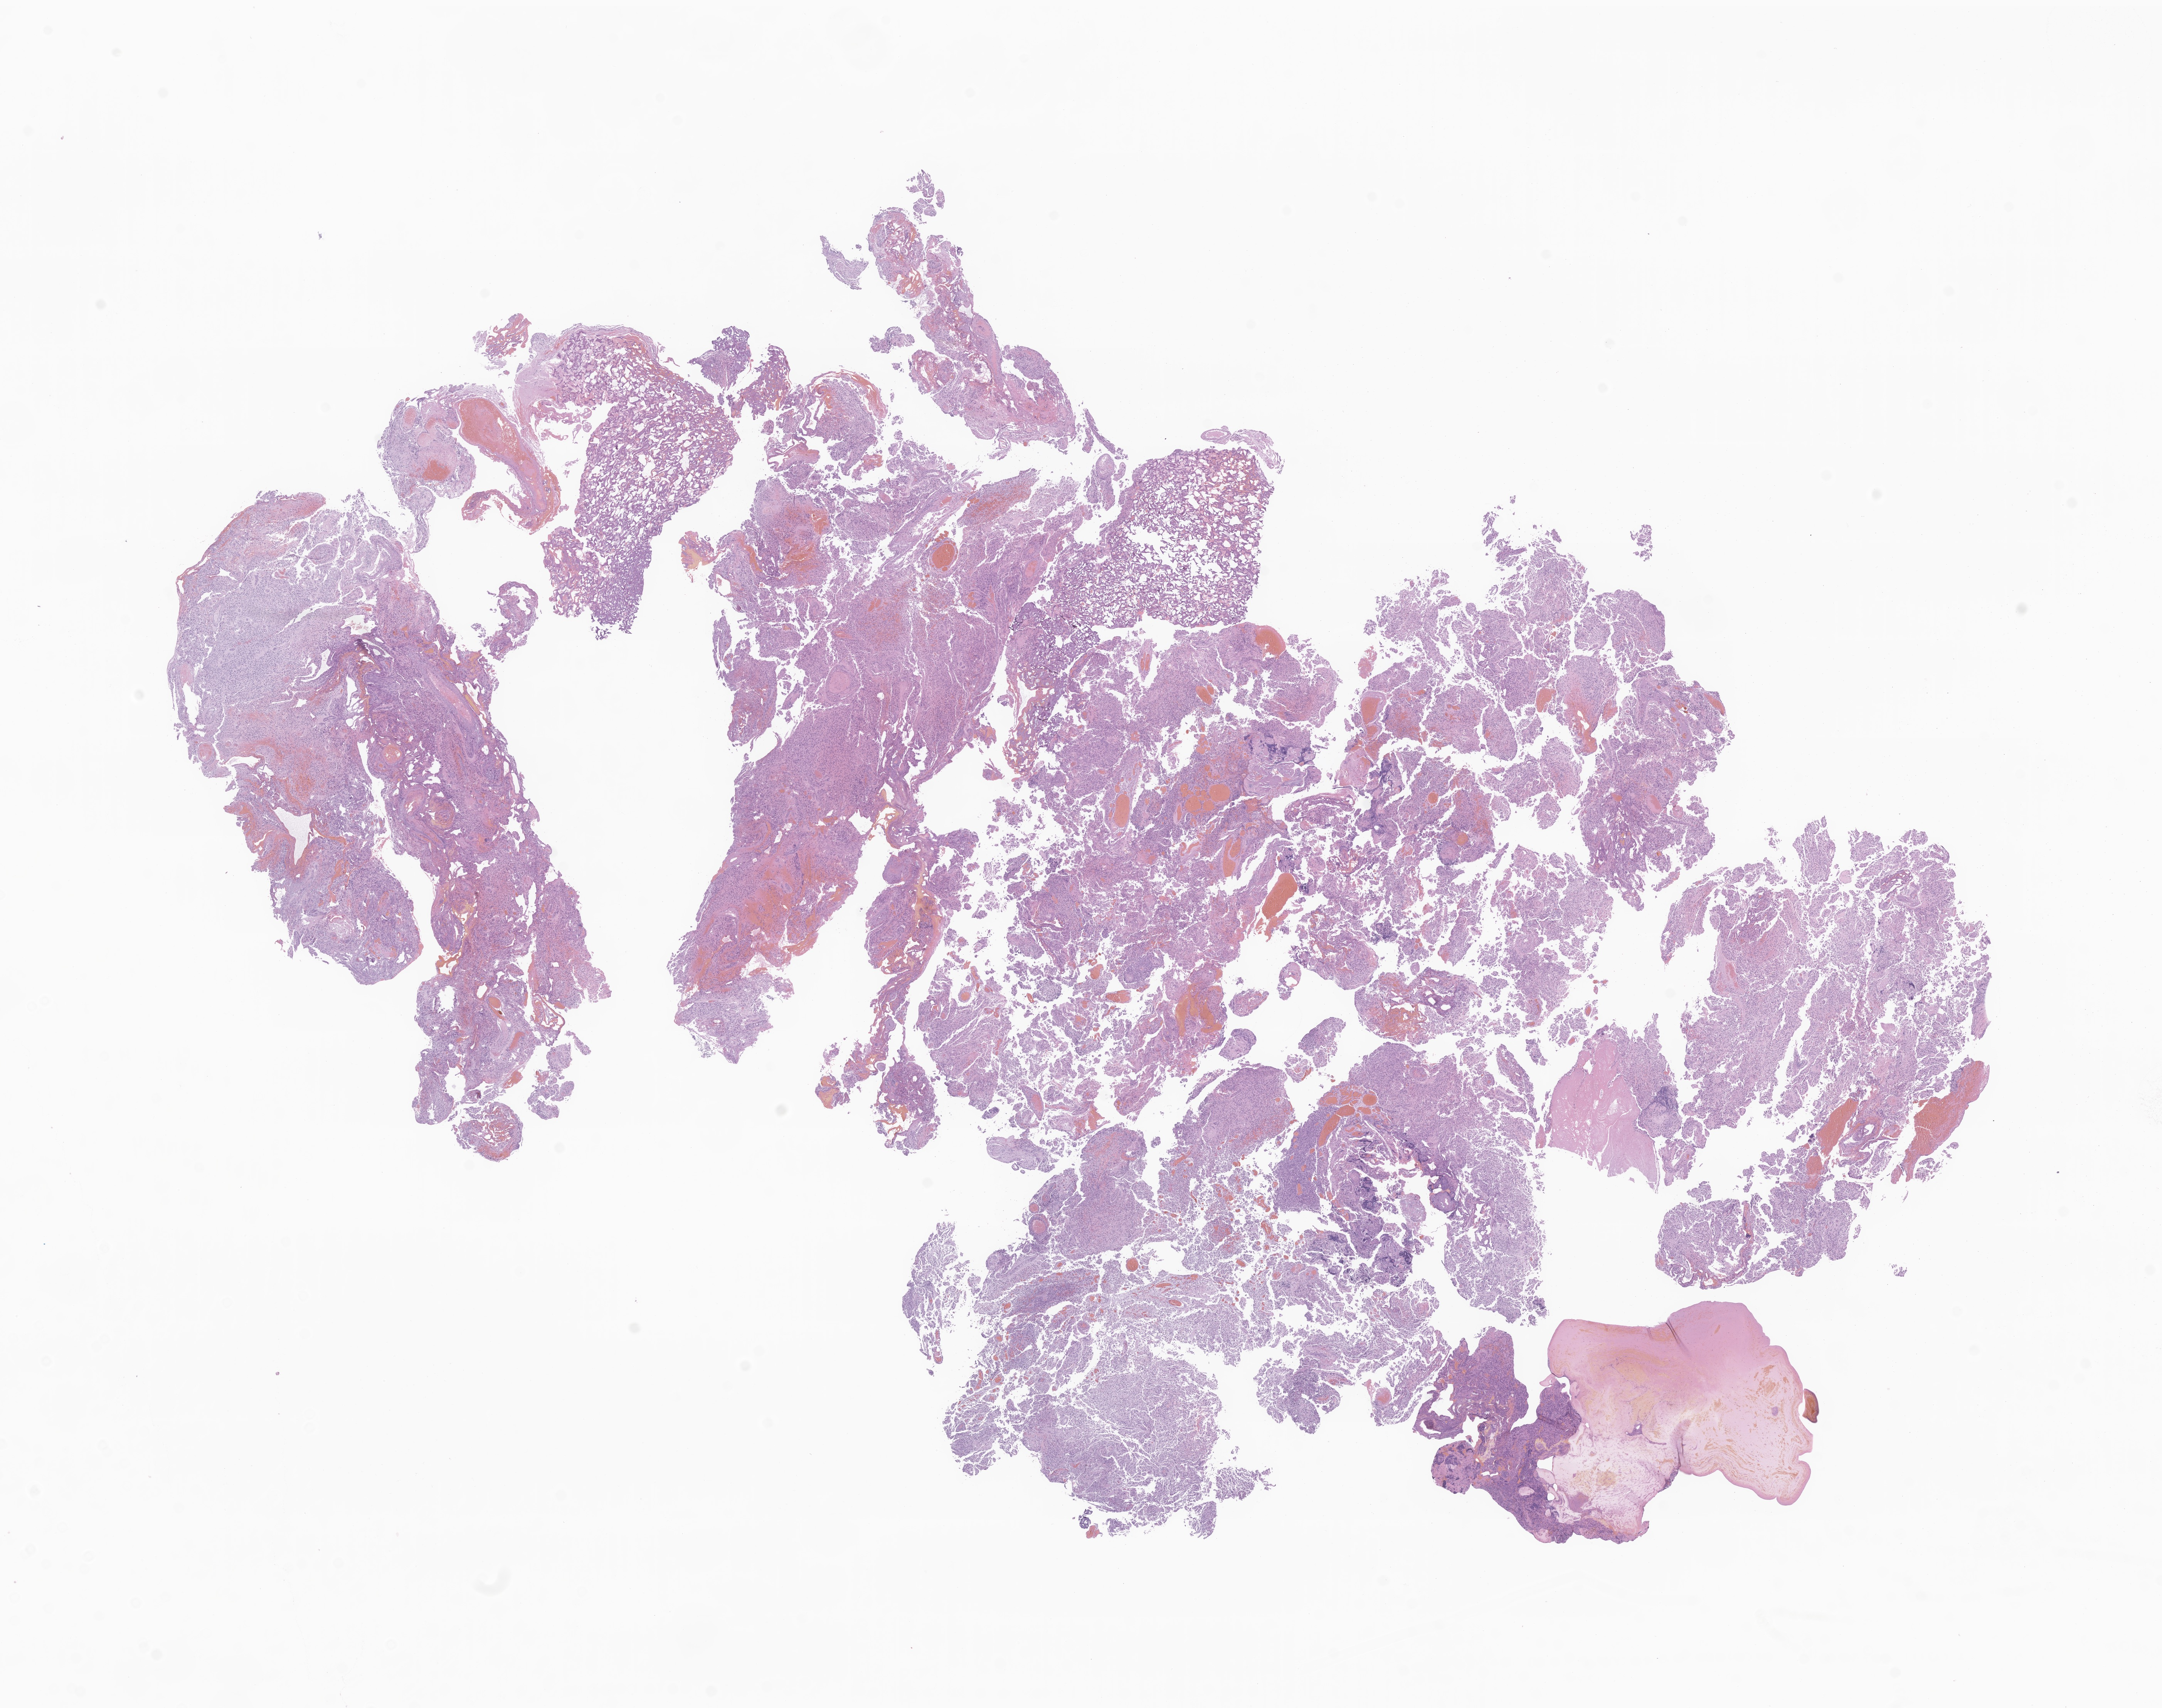
Digitized H&E-stained section of tumor tissue from the spinal cord — low-resolution overview of the scanned area, about 23.6 x 18.7 mm; FFPE section. Male patient, age 249 months (20 years 9 months).
Recorded diagnosis: Ependymoma, NOS.